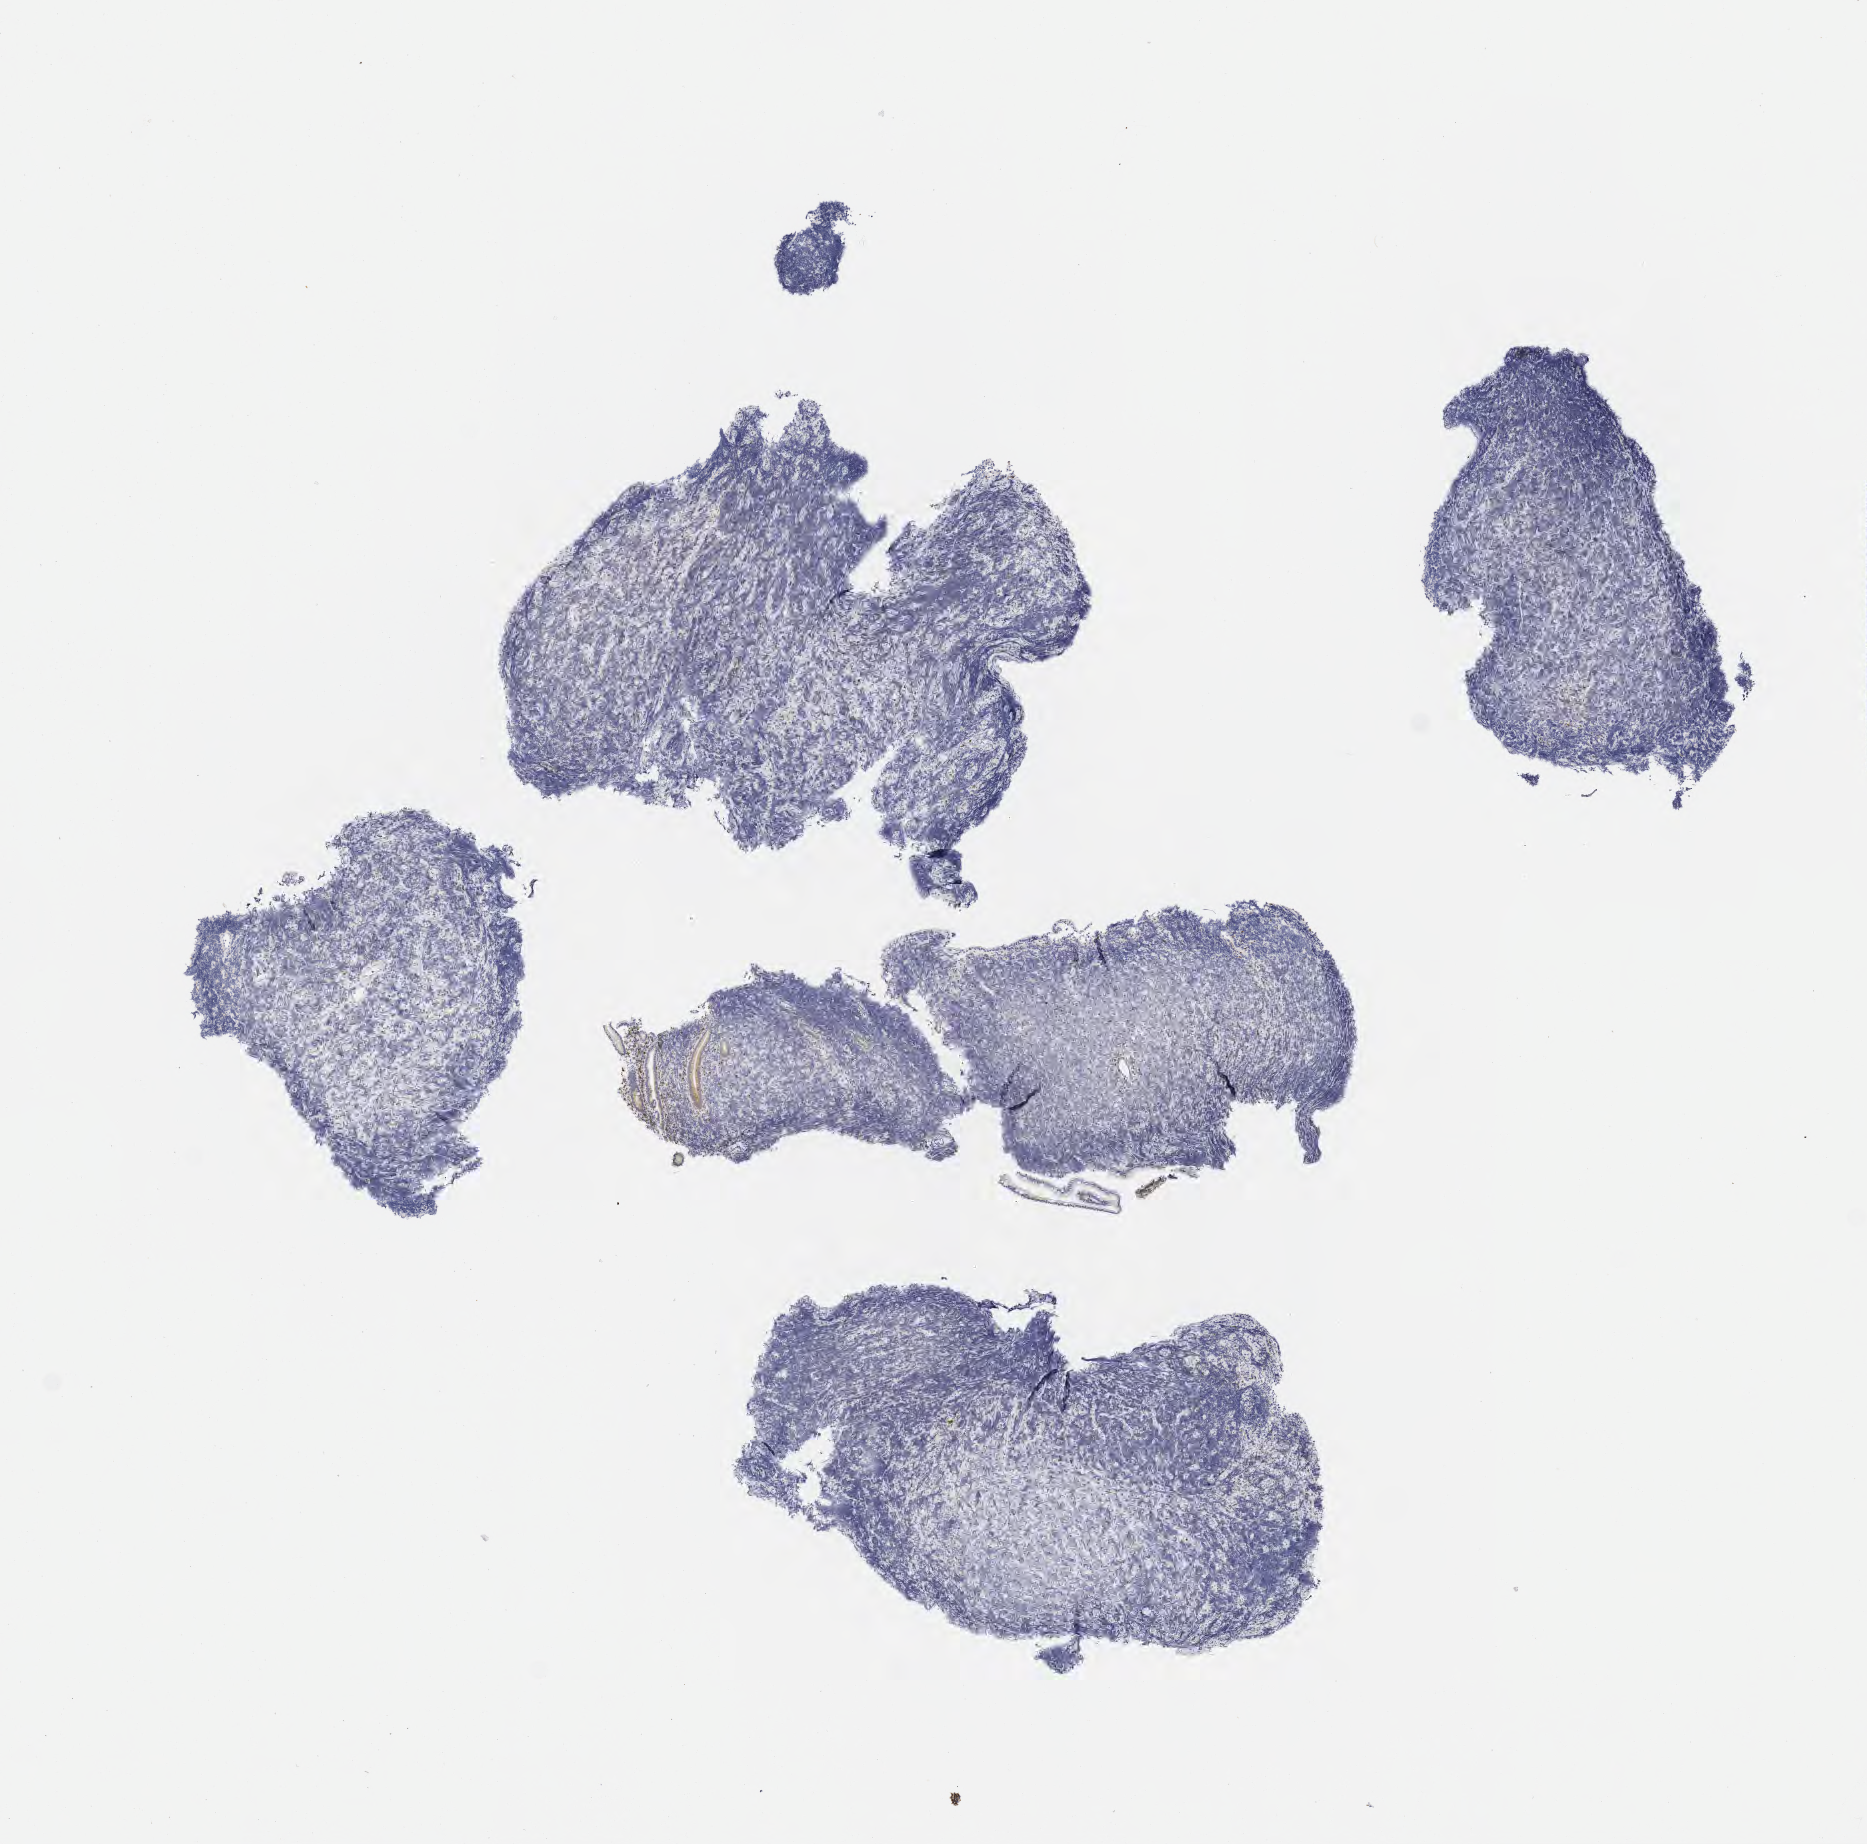
Immunohistochemistry (IHC) whole-slide image stained for BCL2 — whole scanned area (about 7.6 x 7.5 mm) shown as a low-resolution overview. Specimen: tumor tissue. Anatomic site: small intestine. Patient: female, 47 years old.
Histologic diagnosis: Burkitt lymphoma, NOS.